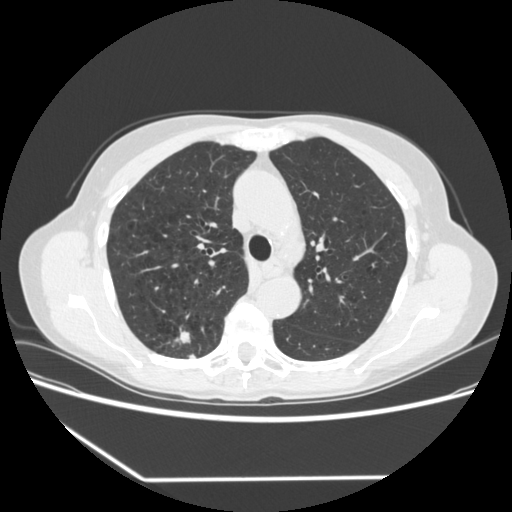
Chest CT (low-dose screening protocol), one axial image; first (baseline) screen; lung window (W 1500 / L -600 HU); 1.25 mm slice thickness; standard (soft-tissue) reconstruction kernel (STANDARD); 120 kVp; slice 235 of 323 in the series; 512 × 512 image matrix. Female, age 67 years at enrolment. Current smoker at enrolment.
Lesion marked by an expert reader, bounding box (x1, y1, x2, y2) in pixels: (159, 324, 202, 363). The screening reader recorded 2 non-calcified nodules or masses ≥4 mm on this exam (right upper lobe, right lower lobe); which of them this box marks is not recorded. Official screen result: positive, change unspecified: nodule(s) >= 4 mm or enlarging nodule(s), mass(es), or other non-specific abnormalities suspicious for lung cancer.